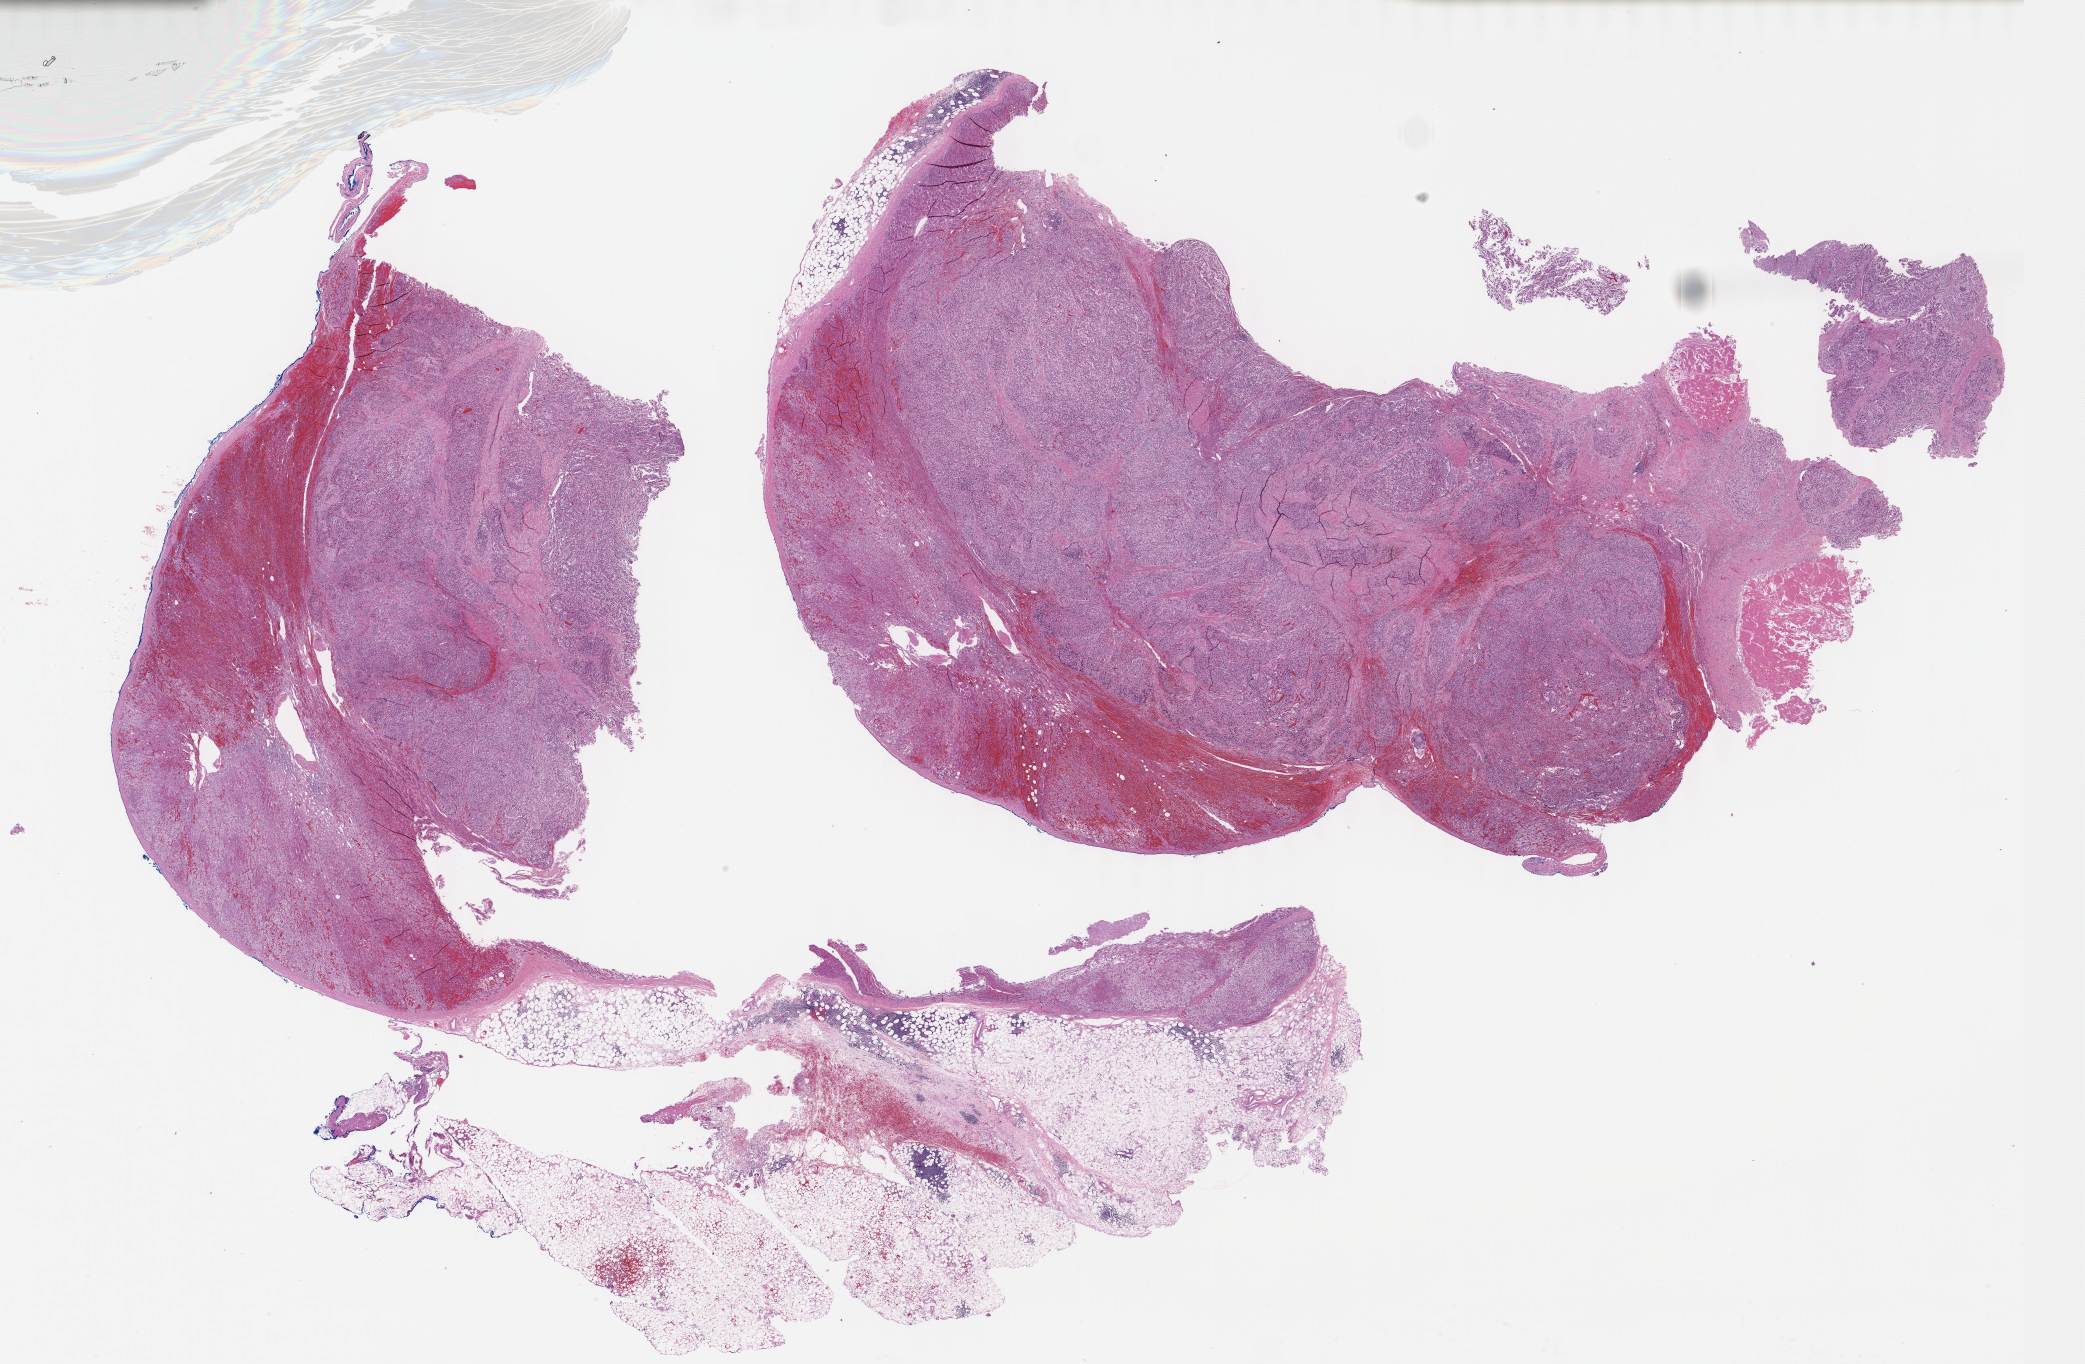
Digitized H&E tissue section (whole slide), whole scanned area (about 33.7 x 22.0 mm, acquisition: 40x scan) shown as a low-resolution overview, formalin-fixed paraffin-embedded (FFPE) diagnostic section, adrenal gland, primary tumour sample. Male, age 67 years at initial diagnosis.
Pathologic diagnosis: Malignant lymphoma, non-Hodgkin, NOS (lymph node, NOS).